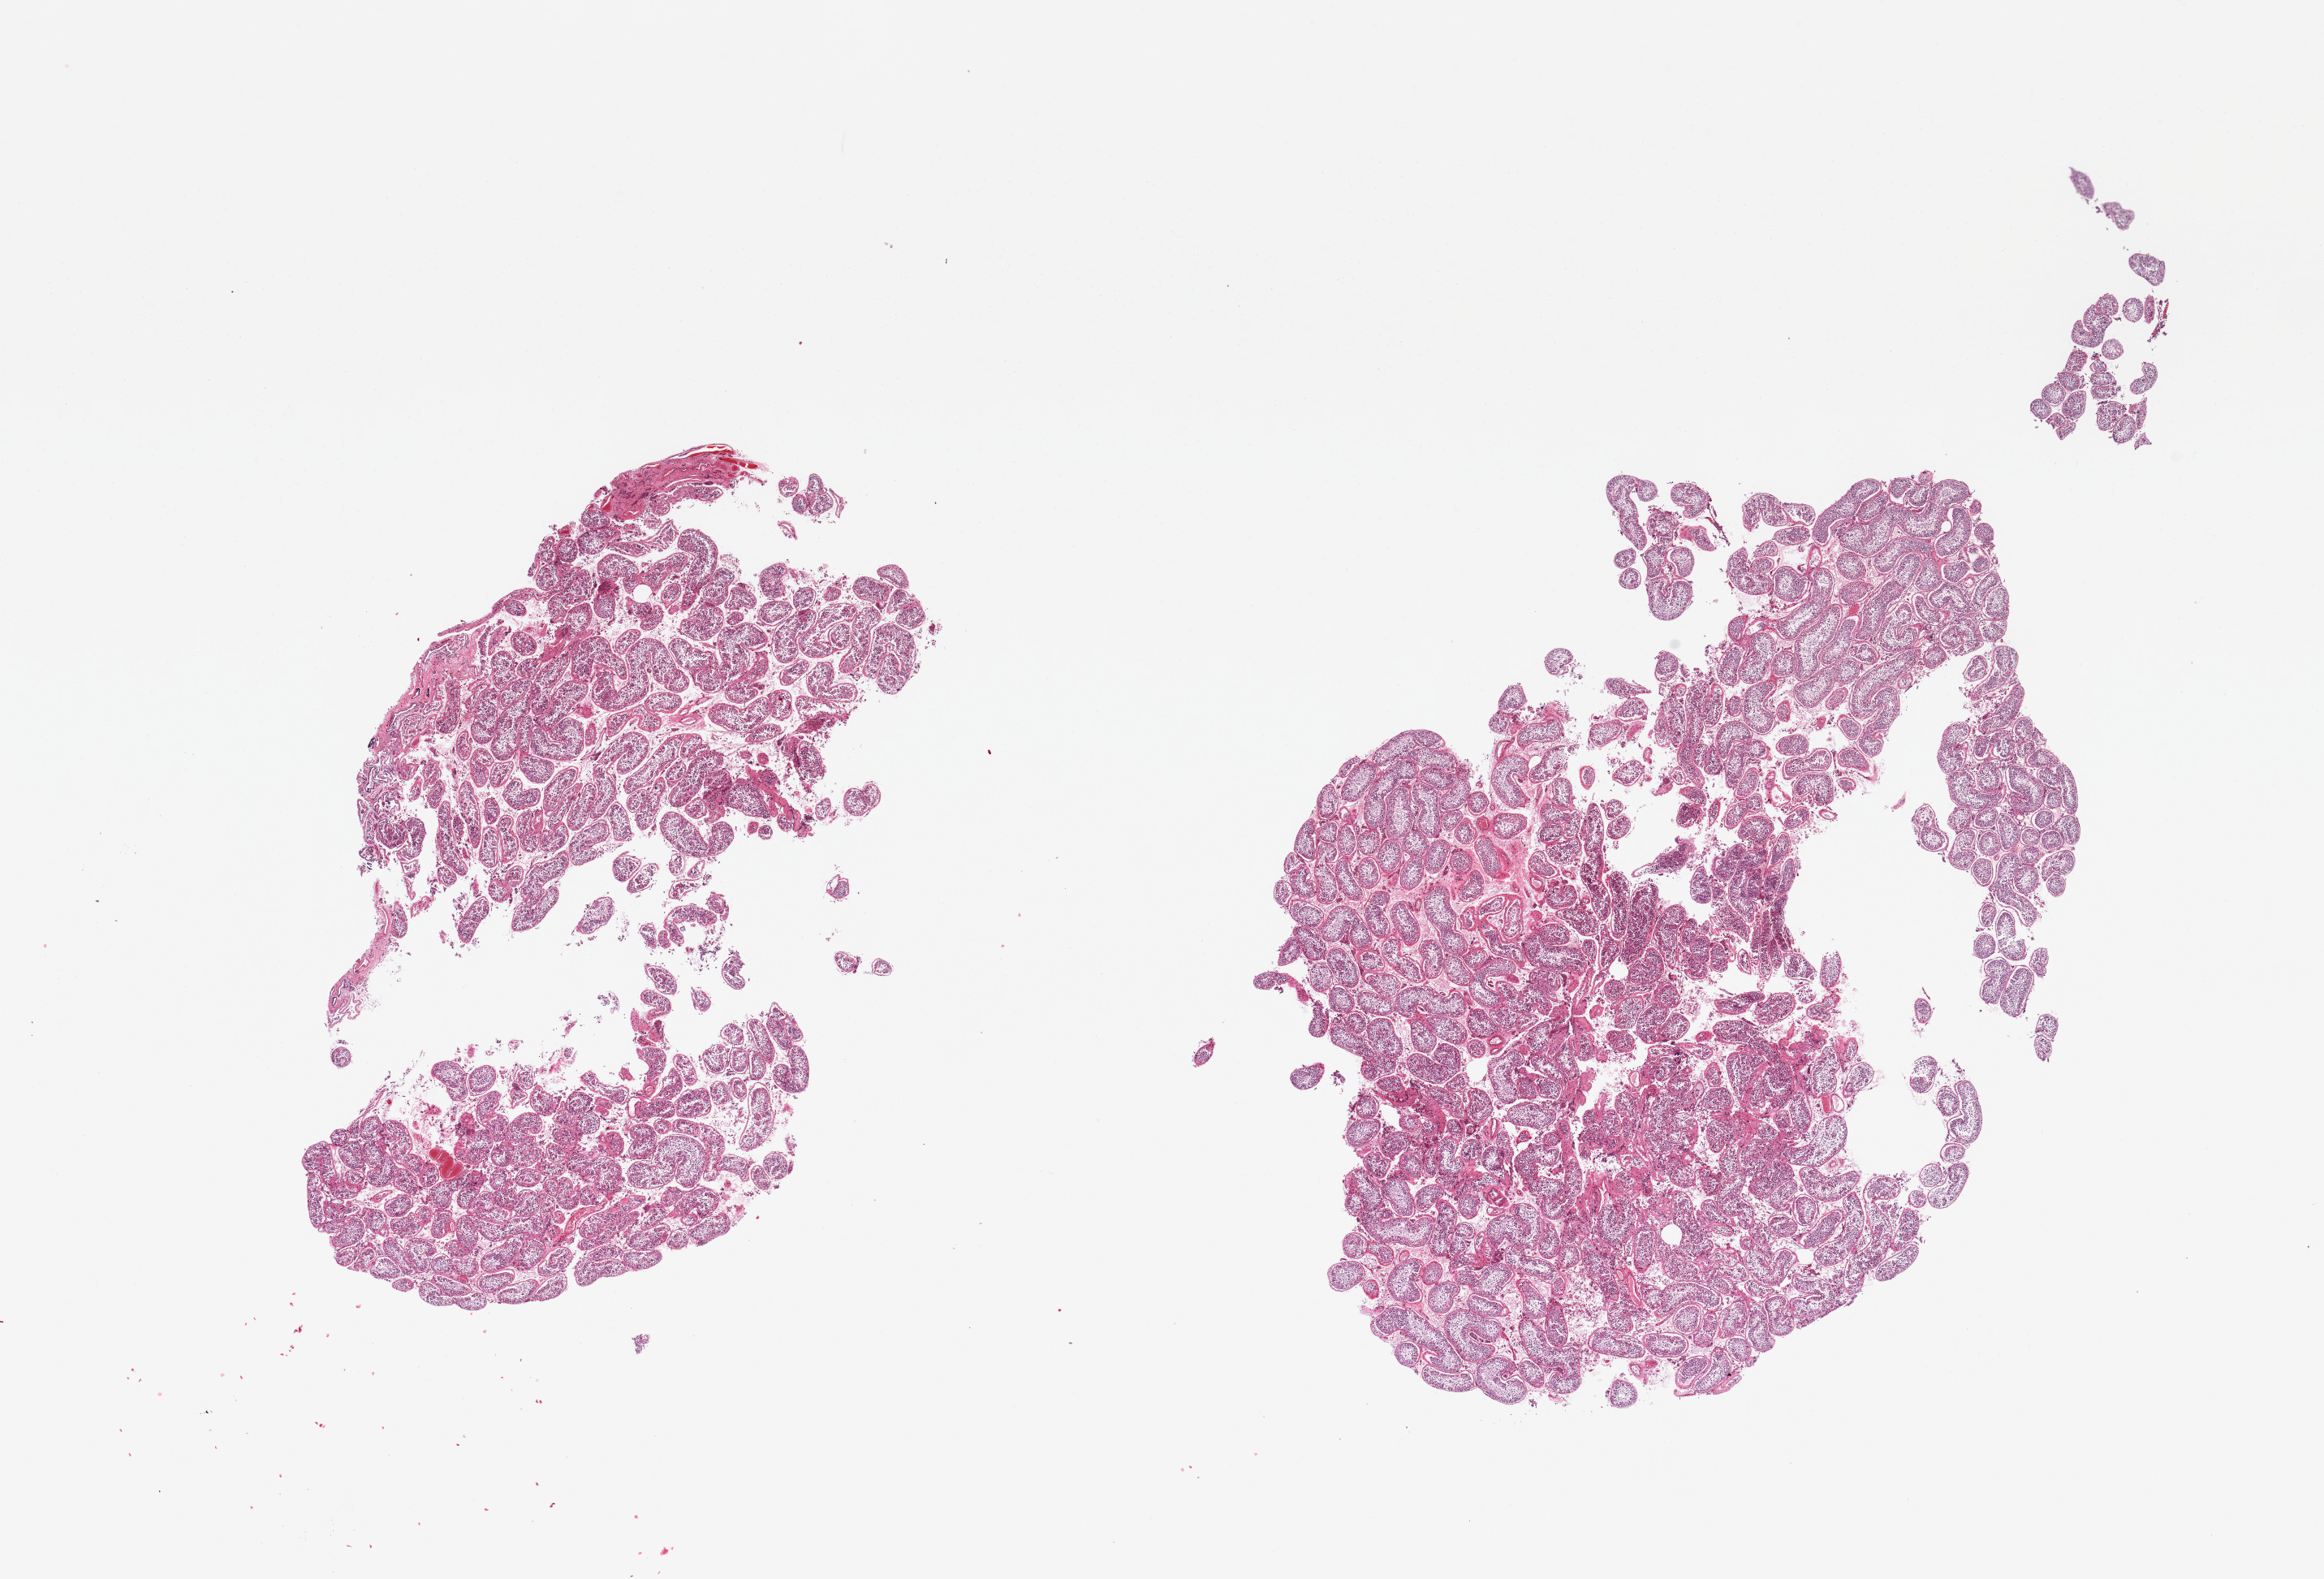
Digitized haematoxylin and eosin-stained section, brightfield — low-resolution overview of the scanned area, about 22.6 x 15.4 mm, PAXgene-fixed paraffin-embedded (PFPE) section, sampled site (target tissue): testis, donor tissue sample.
- reviewer comment on this tissue sample: 2 pieces, spermatogenesis appears reduced